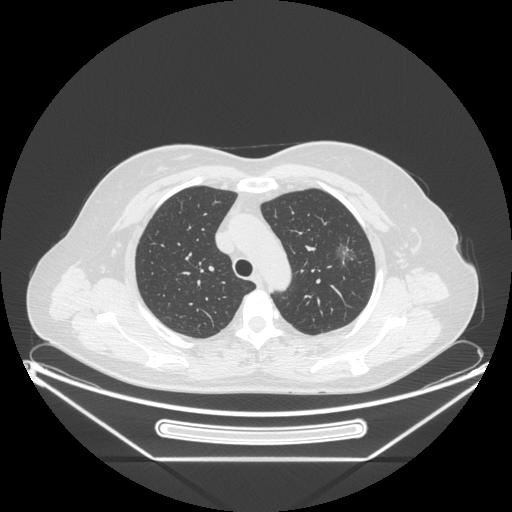
Chest CT, one axial slice. Reconstruction kernel STANDARD. Lung window (W 1500 / L -600 HU). 1.25 mm slice thickness. 512 × 512 image matrix. Patient: female, 54 years. From the clinical record (not read from this slice): clinical TNM (as recorded): T1c N0 M0; histopathological grade: G1.
Structures marked on this image (bounding box drawn by a radiologist):
- lung tumour (recorded histology: adenocarcinoma): bounding box <331,236,360,271> (left, top, right, bottom; pixels)